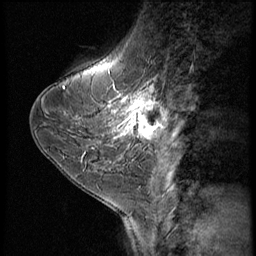
Breast MRI (dynamic contrast-enhanced), one sagittal slice; slice 20 of 56 in the series (ordered by position); dynamic contrast-enhanced series, image 2 of 3 at this slice position (ordered by acquisition); 1.5 T; TE 4.2 ms, TR 9 ms; 2.5 mm slice thickness; 256 × 256 image matrix, field of view 180 × 180 mm. Female patient, age 38 years. From the clinical record (not read from this slice): setting: breast cancer imaged before/during neoadjuvant chemotherapy; receptor status: triple-negative.
Annotated regions visible in this slice (semi-automatically segmented with operator editing):
- analysis volume of interest (the breast-tissue region the enhancement analysis was run in; not a lesion): bounding box [x1, y1, x2, y2] px = [107, 95, 169, 149]
- tumour enhancement mask (voxels above the 140 % enhancement threshold inside the analysis volume of interest): [112, 95, 167, 139]